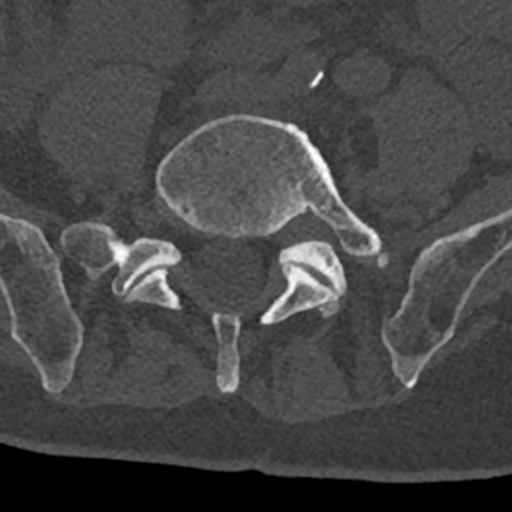
CT including the spine, one axial slice. Slice 187 of 797 in the series (ordered by position). Reconstruction kernel Br40s/3. Bone window (W 1800 / L 400 HU). 0.5 mm slice thickness. 512 × 512 image matrix, field of view 160 × 160 mm. Patient: male, 74 years. Case-level facts recorded for this patient, not image findings: primary cancer: renal; vertebrae with lytic lesions (as recorded): T10, L1, L2, L3, L4, L5.
Outlined on this slice (semi-automatic segmentation, software-assisted and operator-edited):
- L4 vertebra: bounding box <311,71,324,88> (left, top, right, bottom; pixels)
- L5 vertebra: <127,115,385,393>